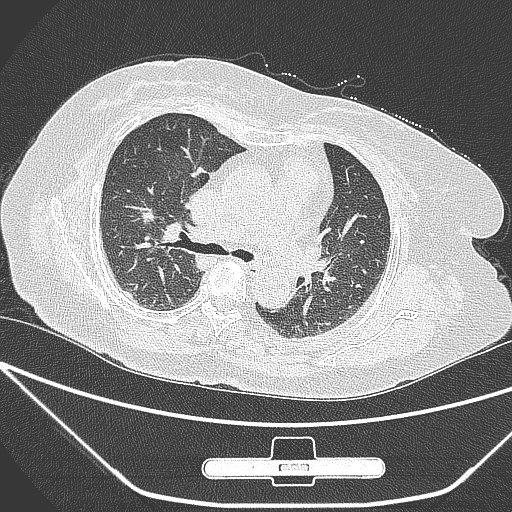
Chest CT, one axial slice; slice 166 of 245 in the series (ordered by position); 120 kVp; lung window (W 1500 / L -600 HU); 512 × 512 image matrix. Female patient, age 65 years. From the clinical record (not read from this slice): clinical TNM (as recorded): T1c N0 M0; histopathological grade: G3.
Structures marked on this image (bounding box drawn by a radiologist):
- lung tumour (recorded histology: adenocarcinoma): bounding box <135,203,152,230> (left, top, right, bottom; pixels)